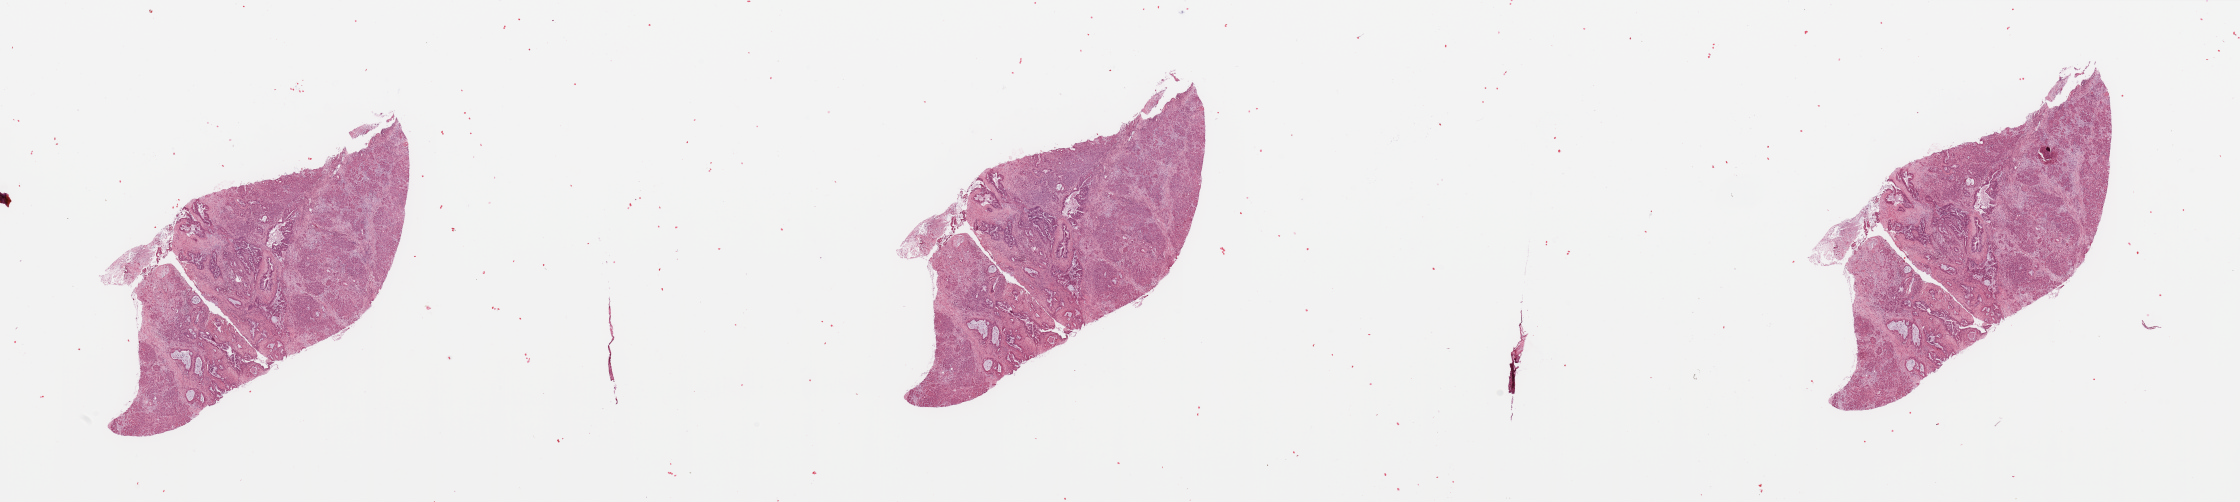
Digitized Hematoxylin and eosin (H&E) stained tissue section (whole slide) — a low-resolution overview of the entire scanned area, about 35.4 x 7.9 mm. Tumour tissue sample, sampled site: pancreas. Male, 73 y/o. Histologic grade: G3 (poorly differentiated). Slide review estimates, as recorded: tumour nuclei 30%, necrosis 5%.
Primary tumour site (as recorded): head. Diagnosis: Infiltrating duct carcinoma, NOS. AJCC pathologic stage: III.